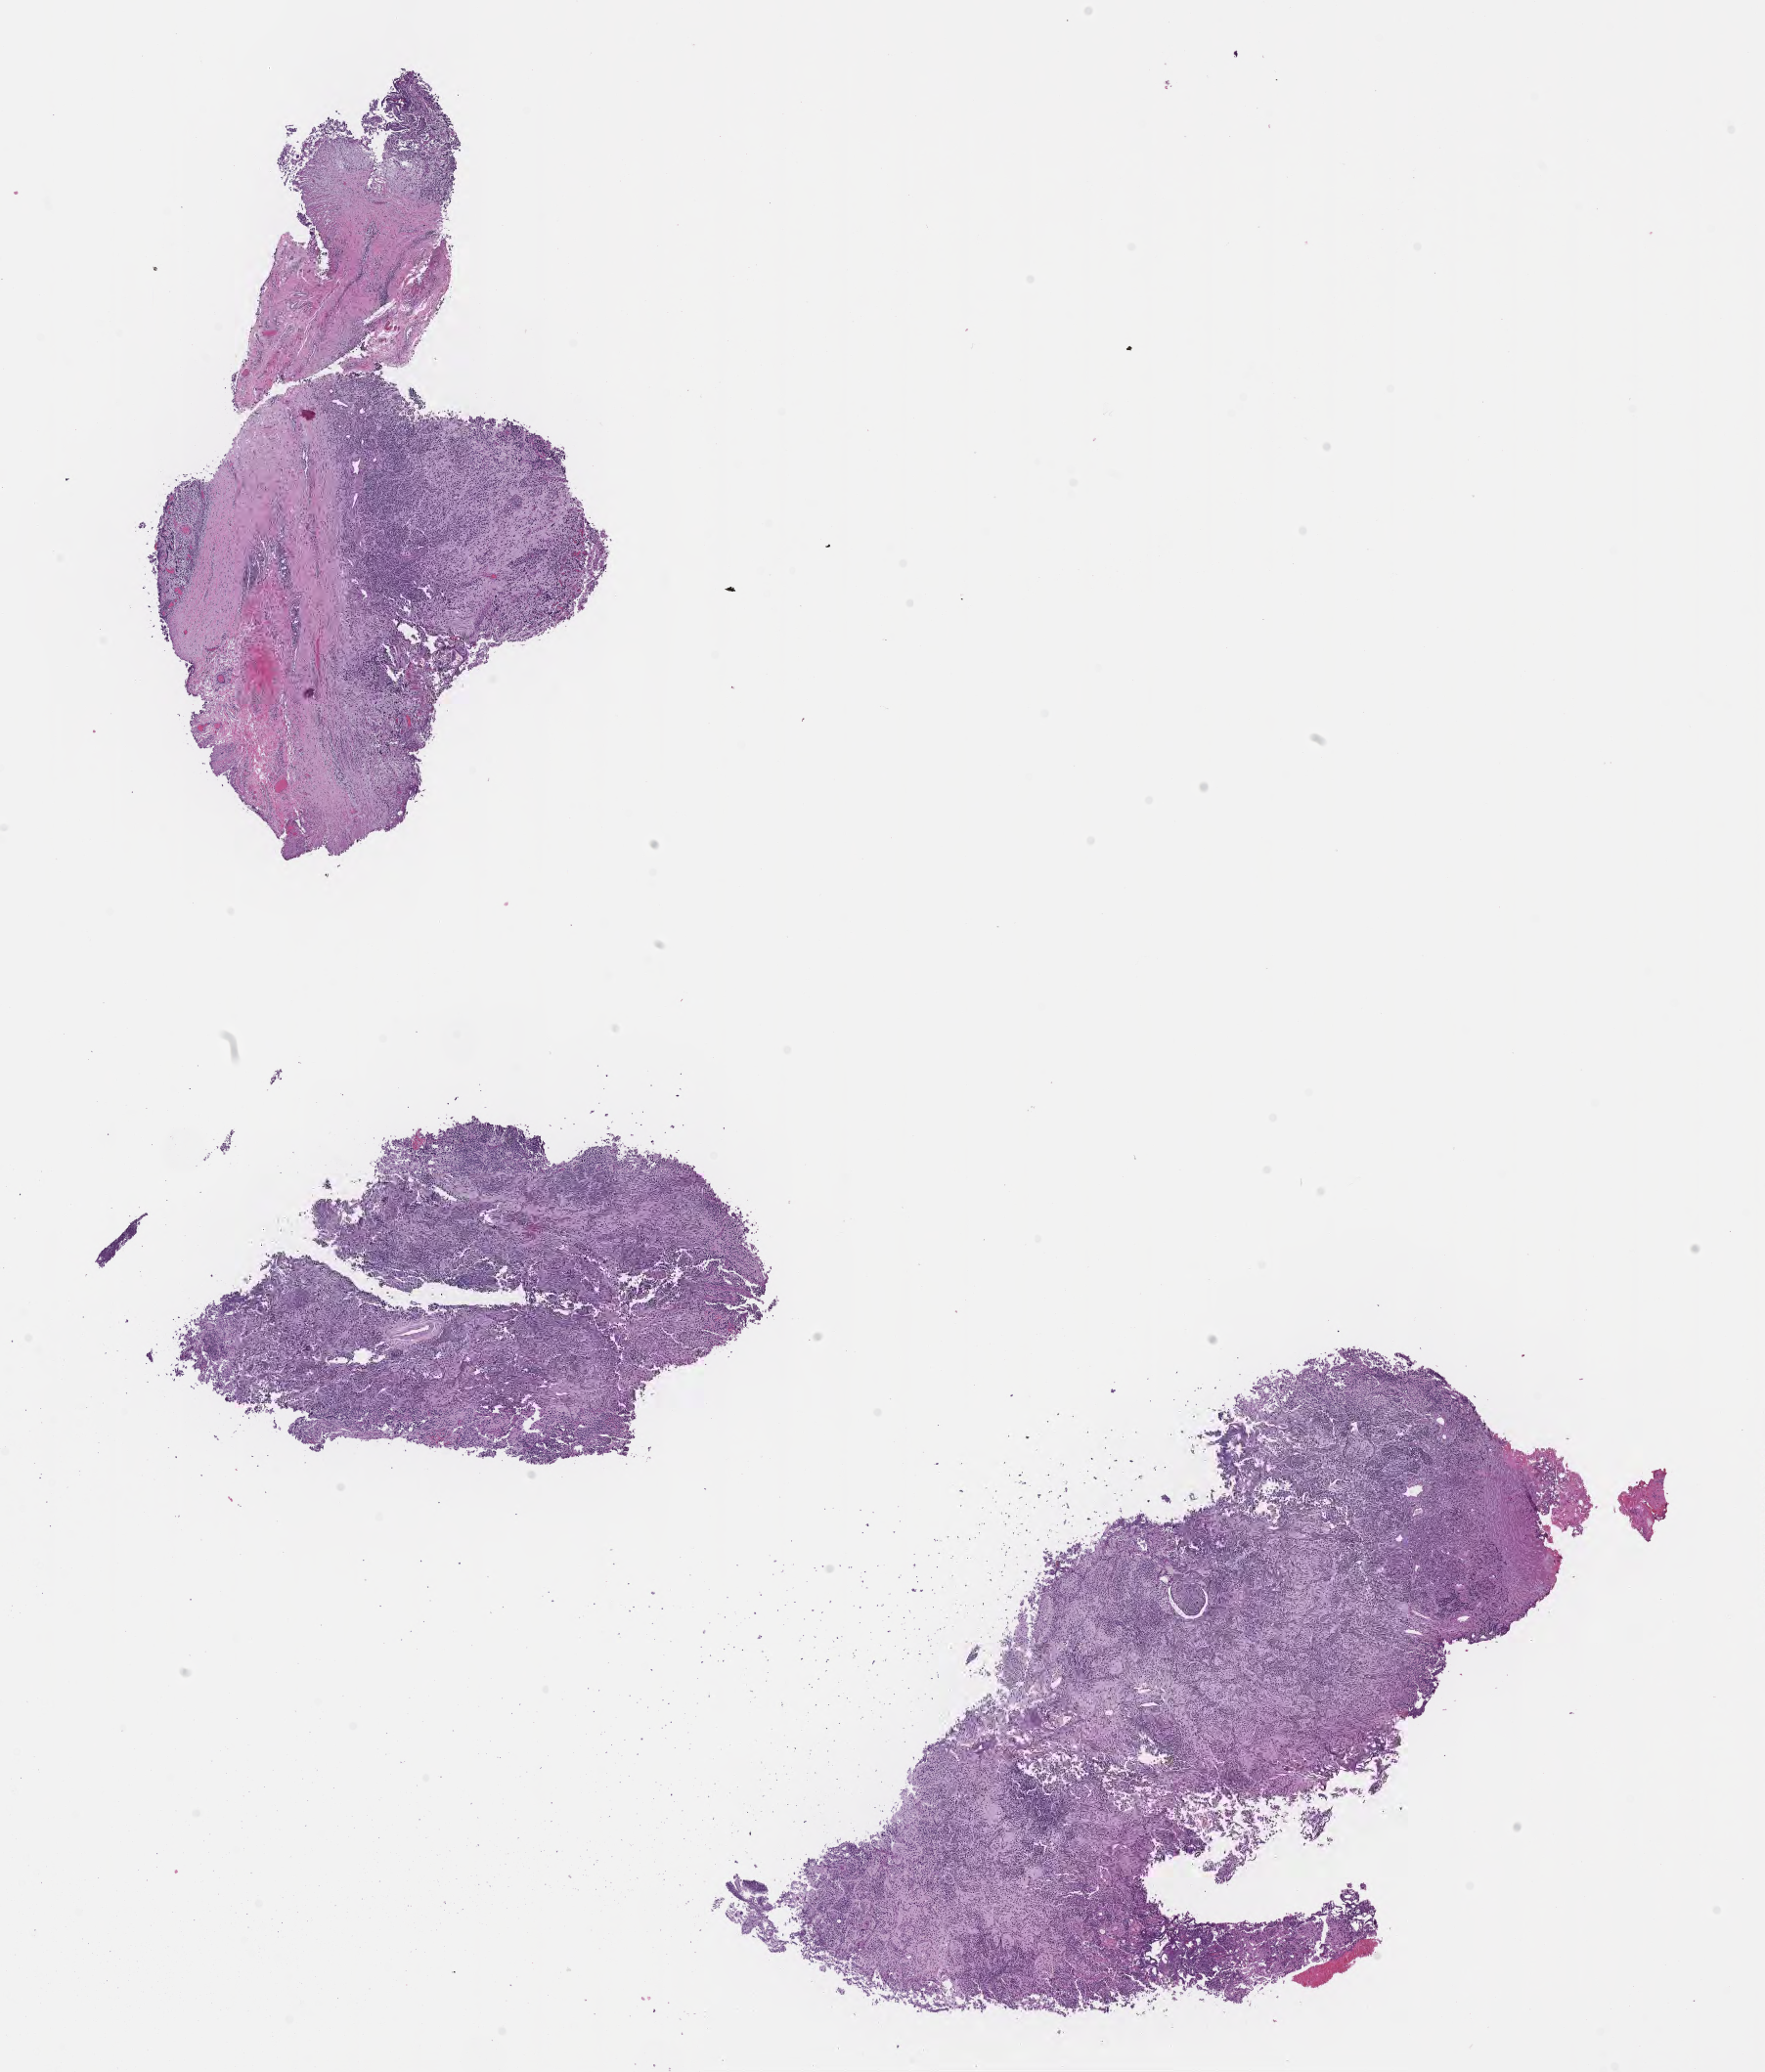
Whole-slide image, H&E stain of tumor tissue from the adrenal gland — shown as a low-resolution overview of the whole scanned area (about 14.6 x 17.1 mm). FFPE section. Male patient, age 214 days.
- diagnosis (ICD-O-3 morphology term): Neuroblastoma, NOS